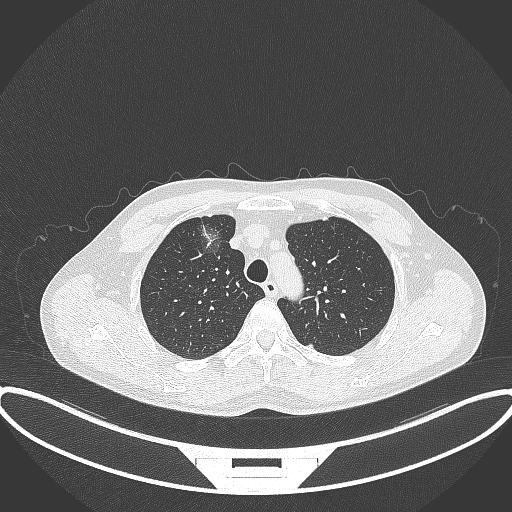
Chest CT, one axial slice; position 287 of 395 along the scan axis; lung window (W 1500 / L -600 HU); 1 mm slice thickness; 512 × 512 image matrix, field of view 424 × 424 mm. Patient: male, 60 years. From the clinical record (not read from this slice): clinical TNM (as recorded): T1c N0 M0.
Annotated regions visible in this slice (rectangle marked by the reading radiologist):
- lung tumour (recorded histology: adenocarcinoma): bounding box [x1, y1, x2, y2] px = [195, 212, 225, 256]